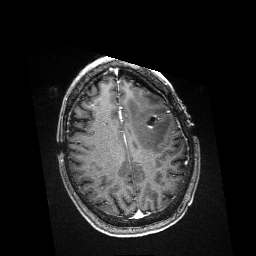
Brain MRI from a brain-tumour surgery series, one axial slice; position 118 of 176 along the scan axis; T1-weighted post-contrast; 256 × 256 image matrix, field of view 256 × 256 mm. Case-level facts recorded for this patient, not image findings: histopathology: Metastatic Melanoma.
Structures marked on this image (manually delineated by an expert):
- residual tumour: bounding box (x1, y1, x2, y2) in pixels: (148, 126, 153, 128)